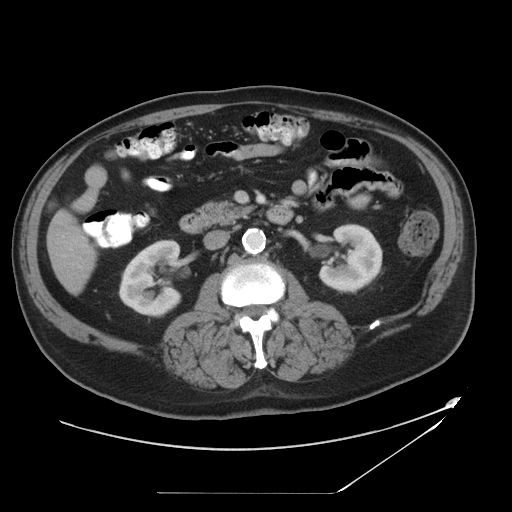
Contrast-enhanced abdominal CT, one axial slice. Position 14 of 49 along the scan axis. Reconstruction kernel STANDARD. 120 kVp. Intravenous contrast given. Soft-tissue window (W 400 / L 40 HU). 5 mm slice thickness. 512 × 512 image matrix. Male patient, age 72 years. From the clinical record (not read from this slice): diagnosis: colorectal cancer liver metastases, imaged before liver resection; multiple liver metastases: no; largest metastasis: 2.5 cm; disease in both lobes: no.
Structures marked on this image (outlined manually by an expert reader):
- liver: bounding box [x1, y1, x2, y2] px = [49, 213, 95, 291]
- planned liver remnant (the part of the liver to remain after resection): [49, 213, 95, 291]